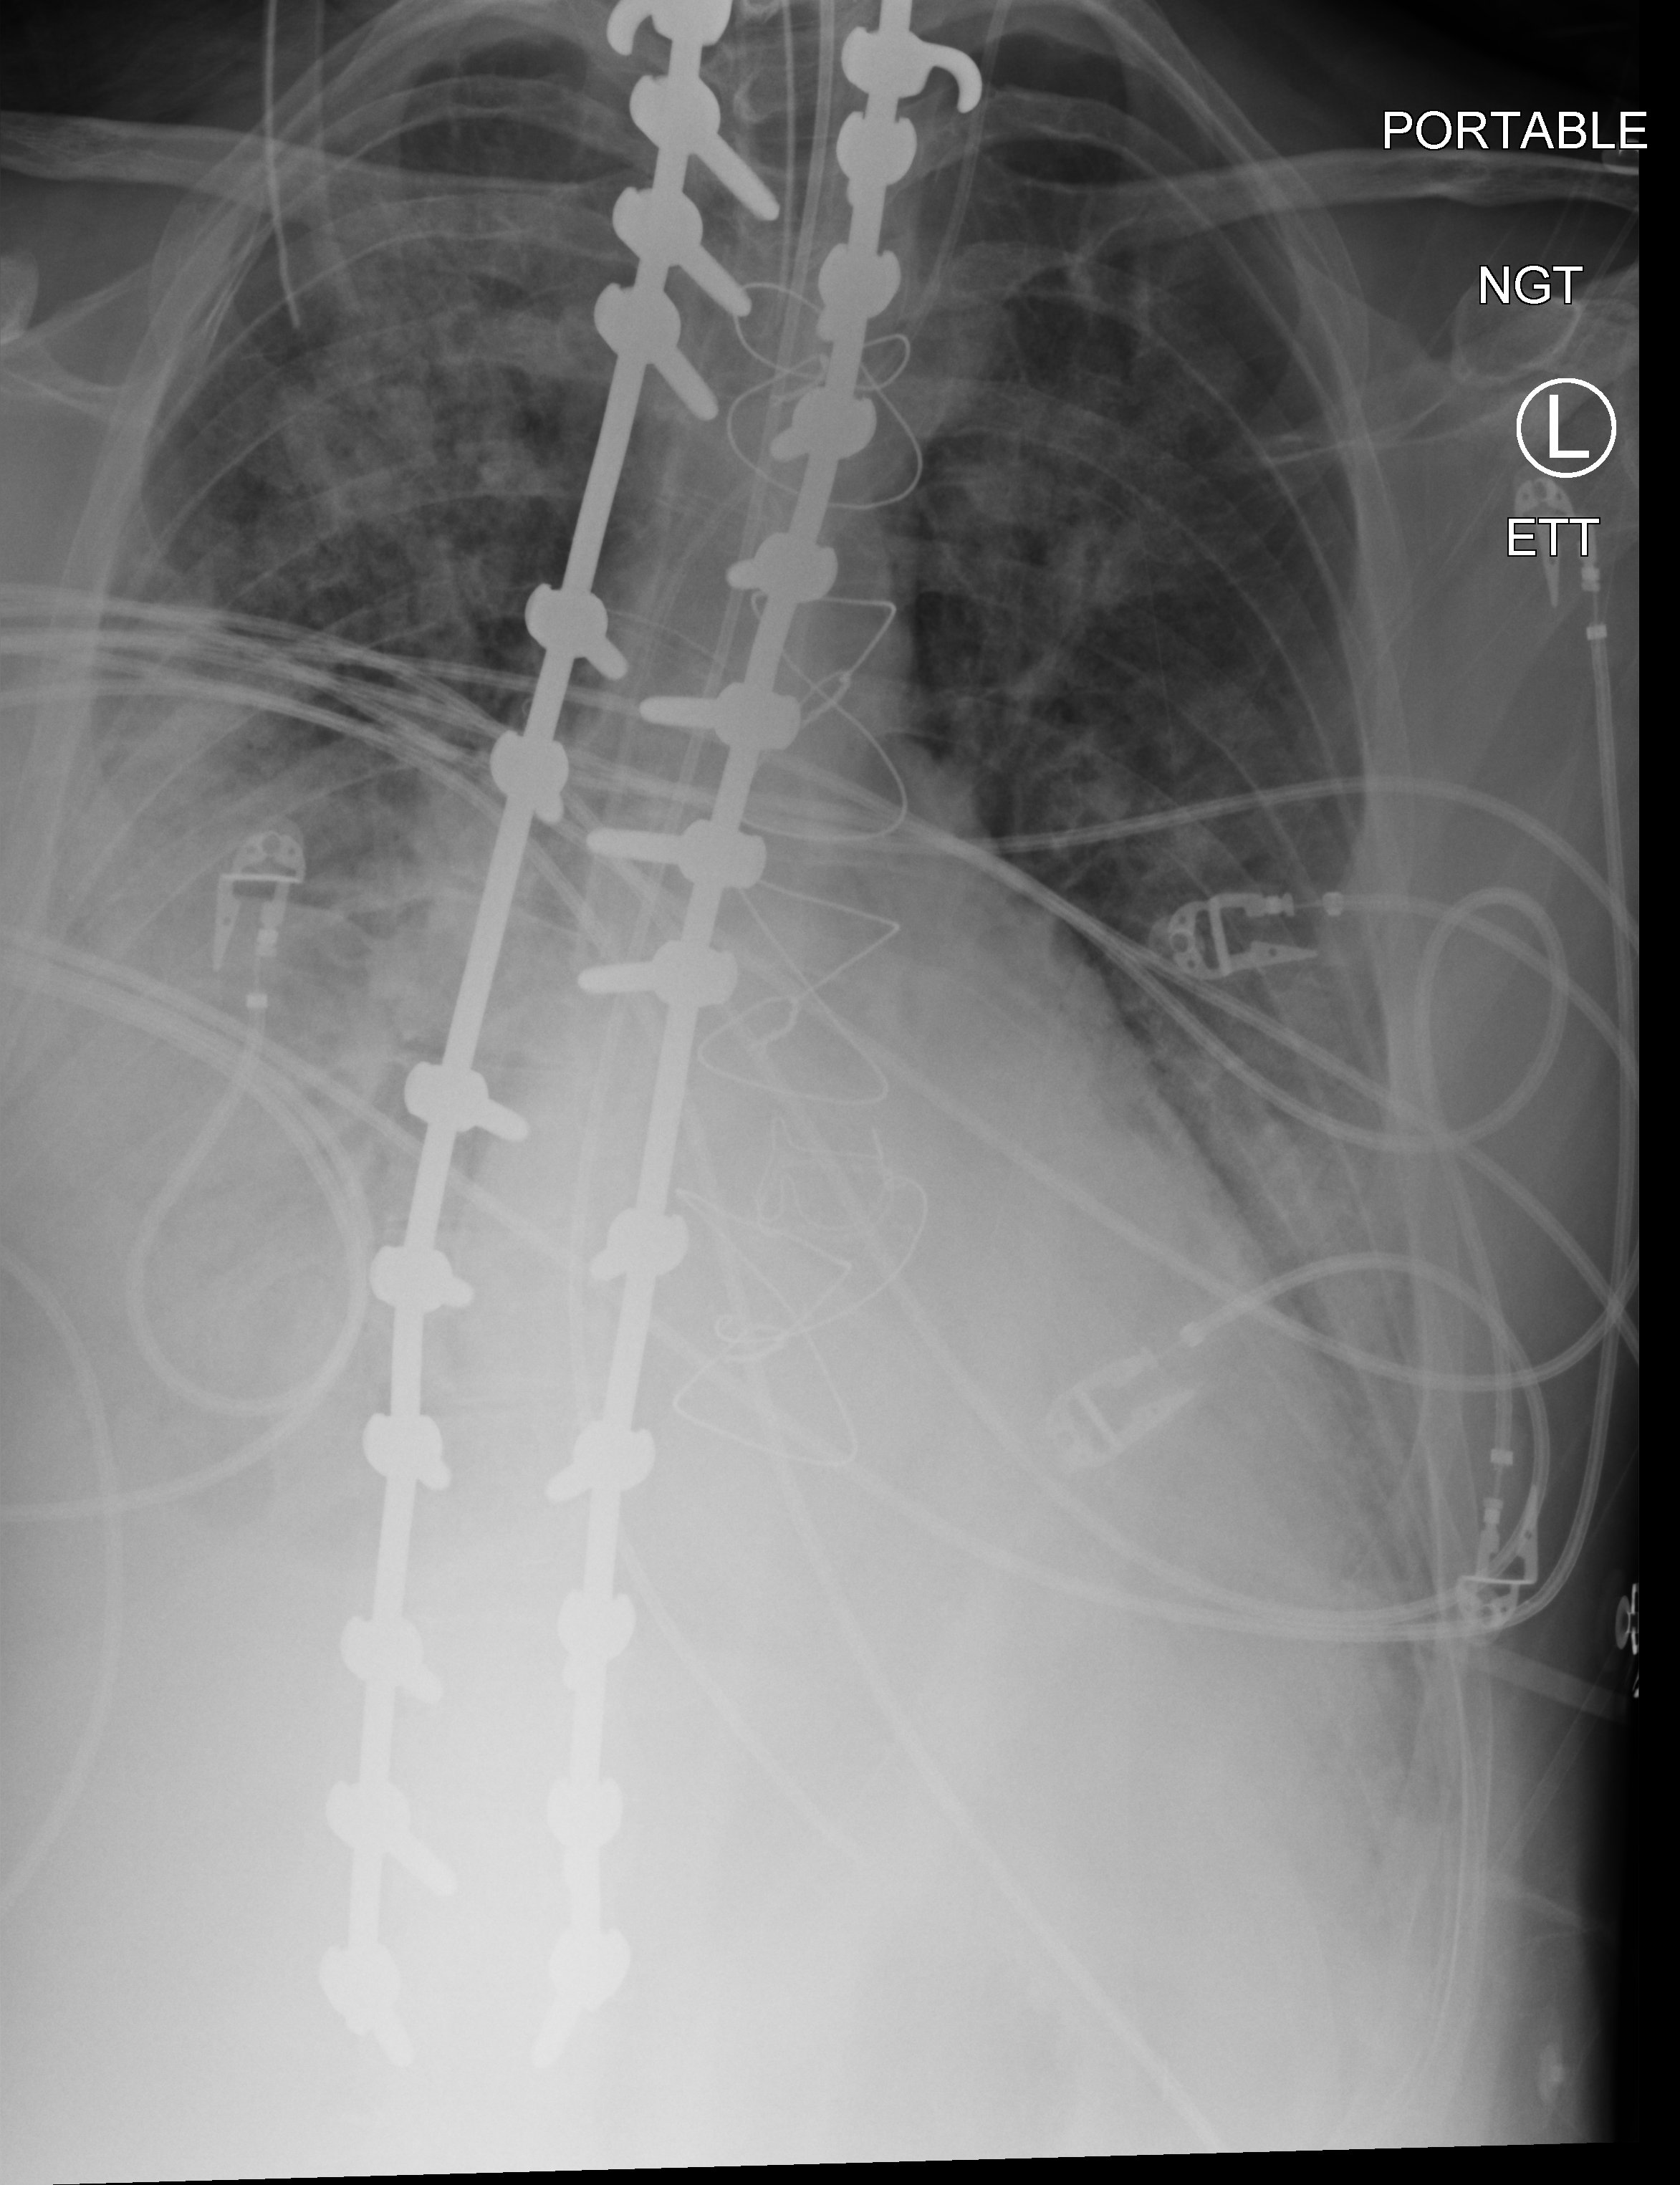
Portable chest radiograph; anteroposterior (AP) projection. Adult patient hospitalised with COVID-19, age 18–59 years.
Hospital-stay facts (about this admission, not read from this image; timing relative to this image not recorded): admitted to intensive care during this hospital stay: yes; length of hospital stay: 15 days; COPD (admission record): no.